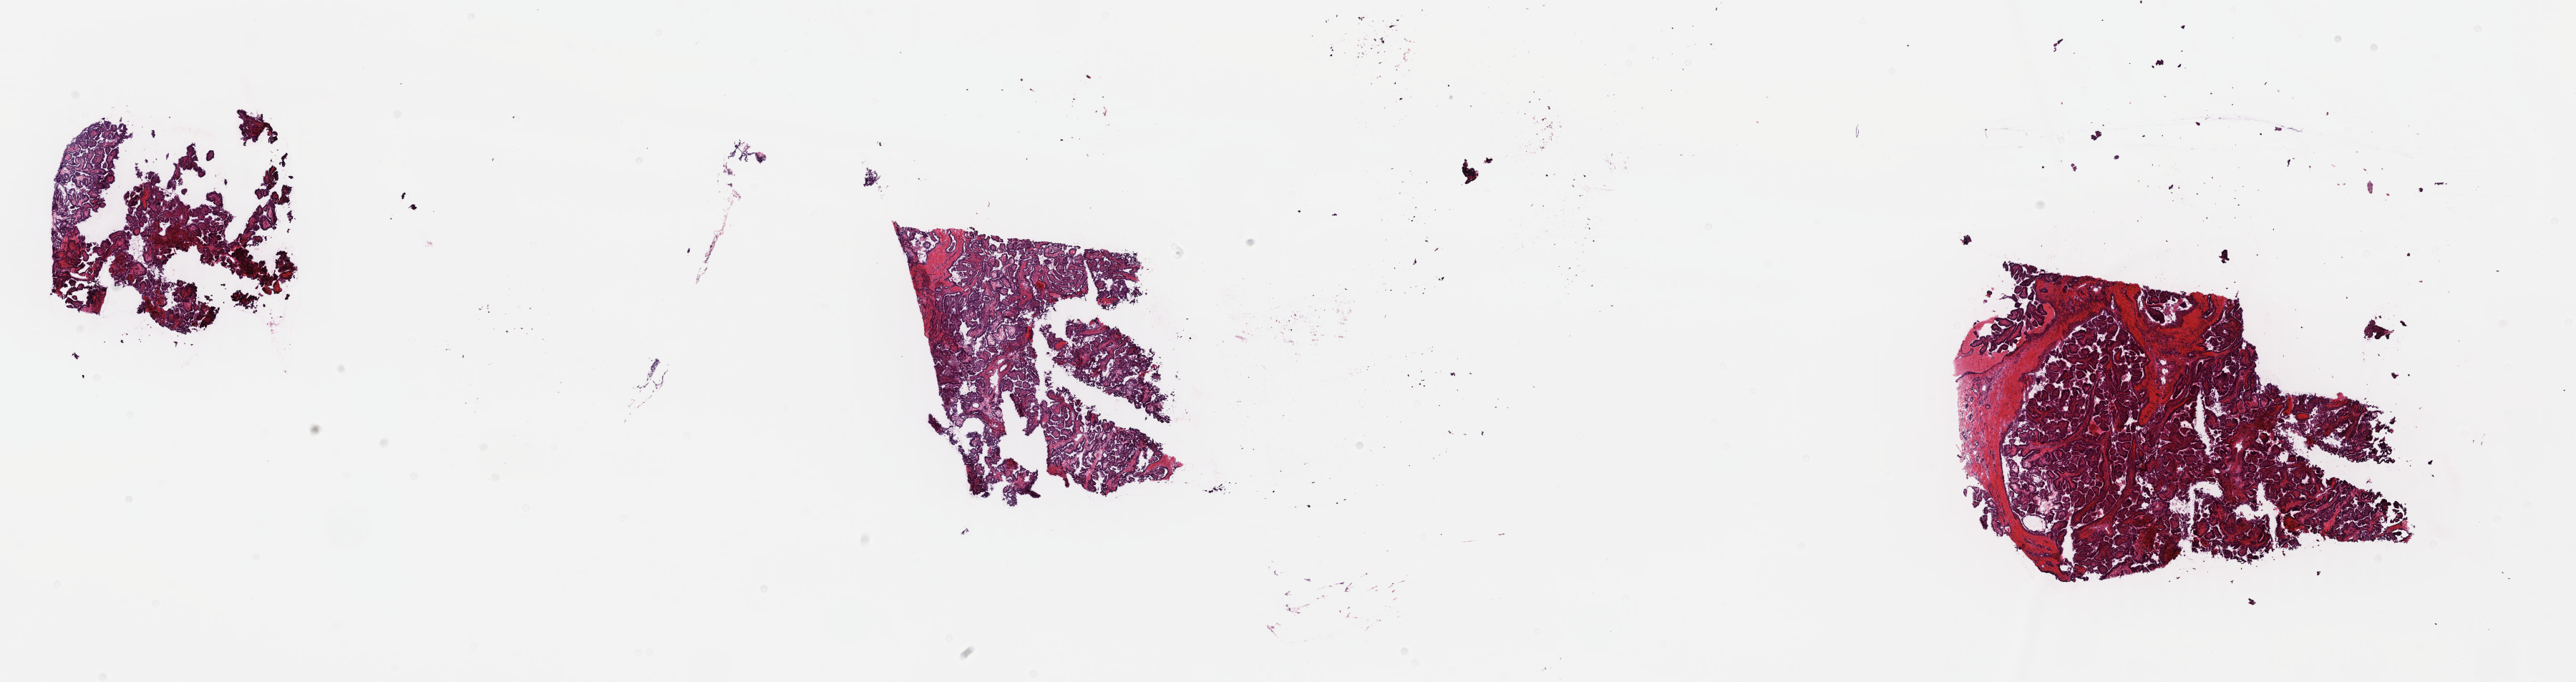
H&E-stained whole-slide image — shown as a low-resolution overview of the whole scanned area (about 28.4 x 7.5 mm, from a 40x scan); frozen section from the top of the tissue portion; primary tumour sample from the thyroid. Female patient; age at initial diagnosis 20 years.
Histologic diagnosis: Papillary adenocarcinoma, NOS (thyroid gland).